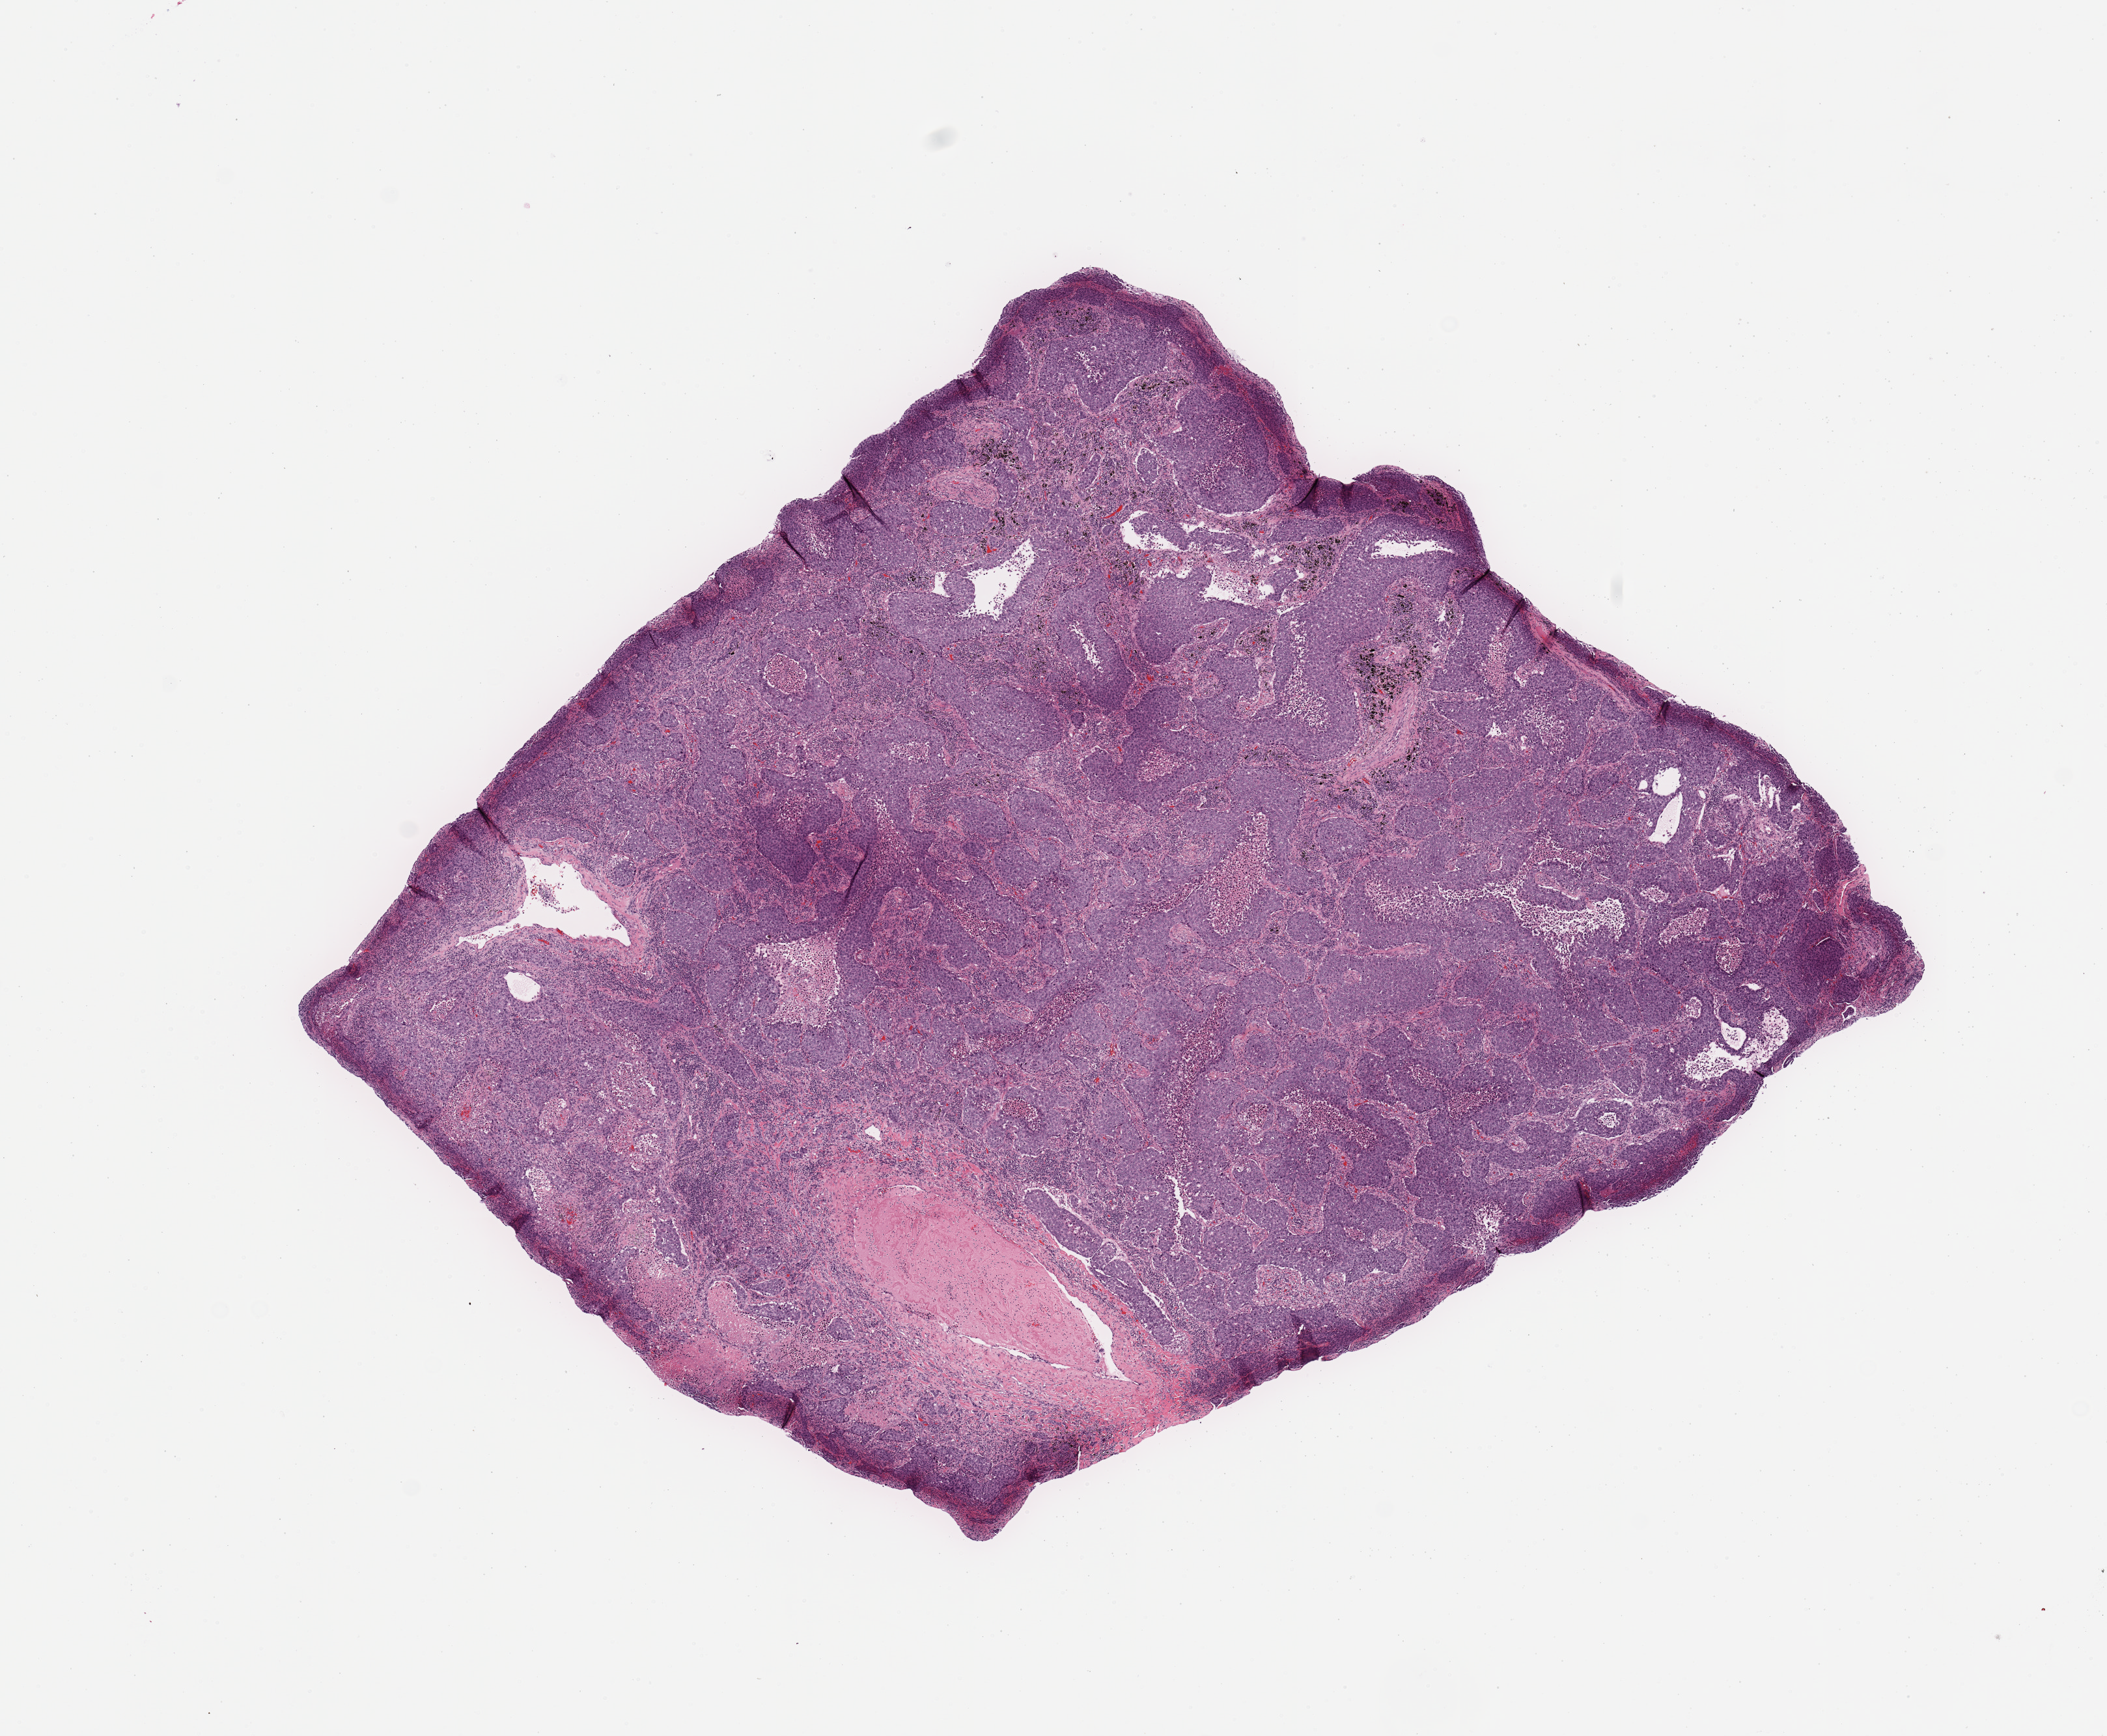
H&E-stained whole-slide image — a low-resolution overview of the entire scanned area, about 12.8 x 10.5 mm (acquisition: 20x scan). Tumour tissue sample, lung. Male, 72 y/o.
Diagnosis: Adenocarcinoma, NOS.